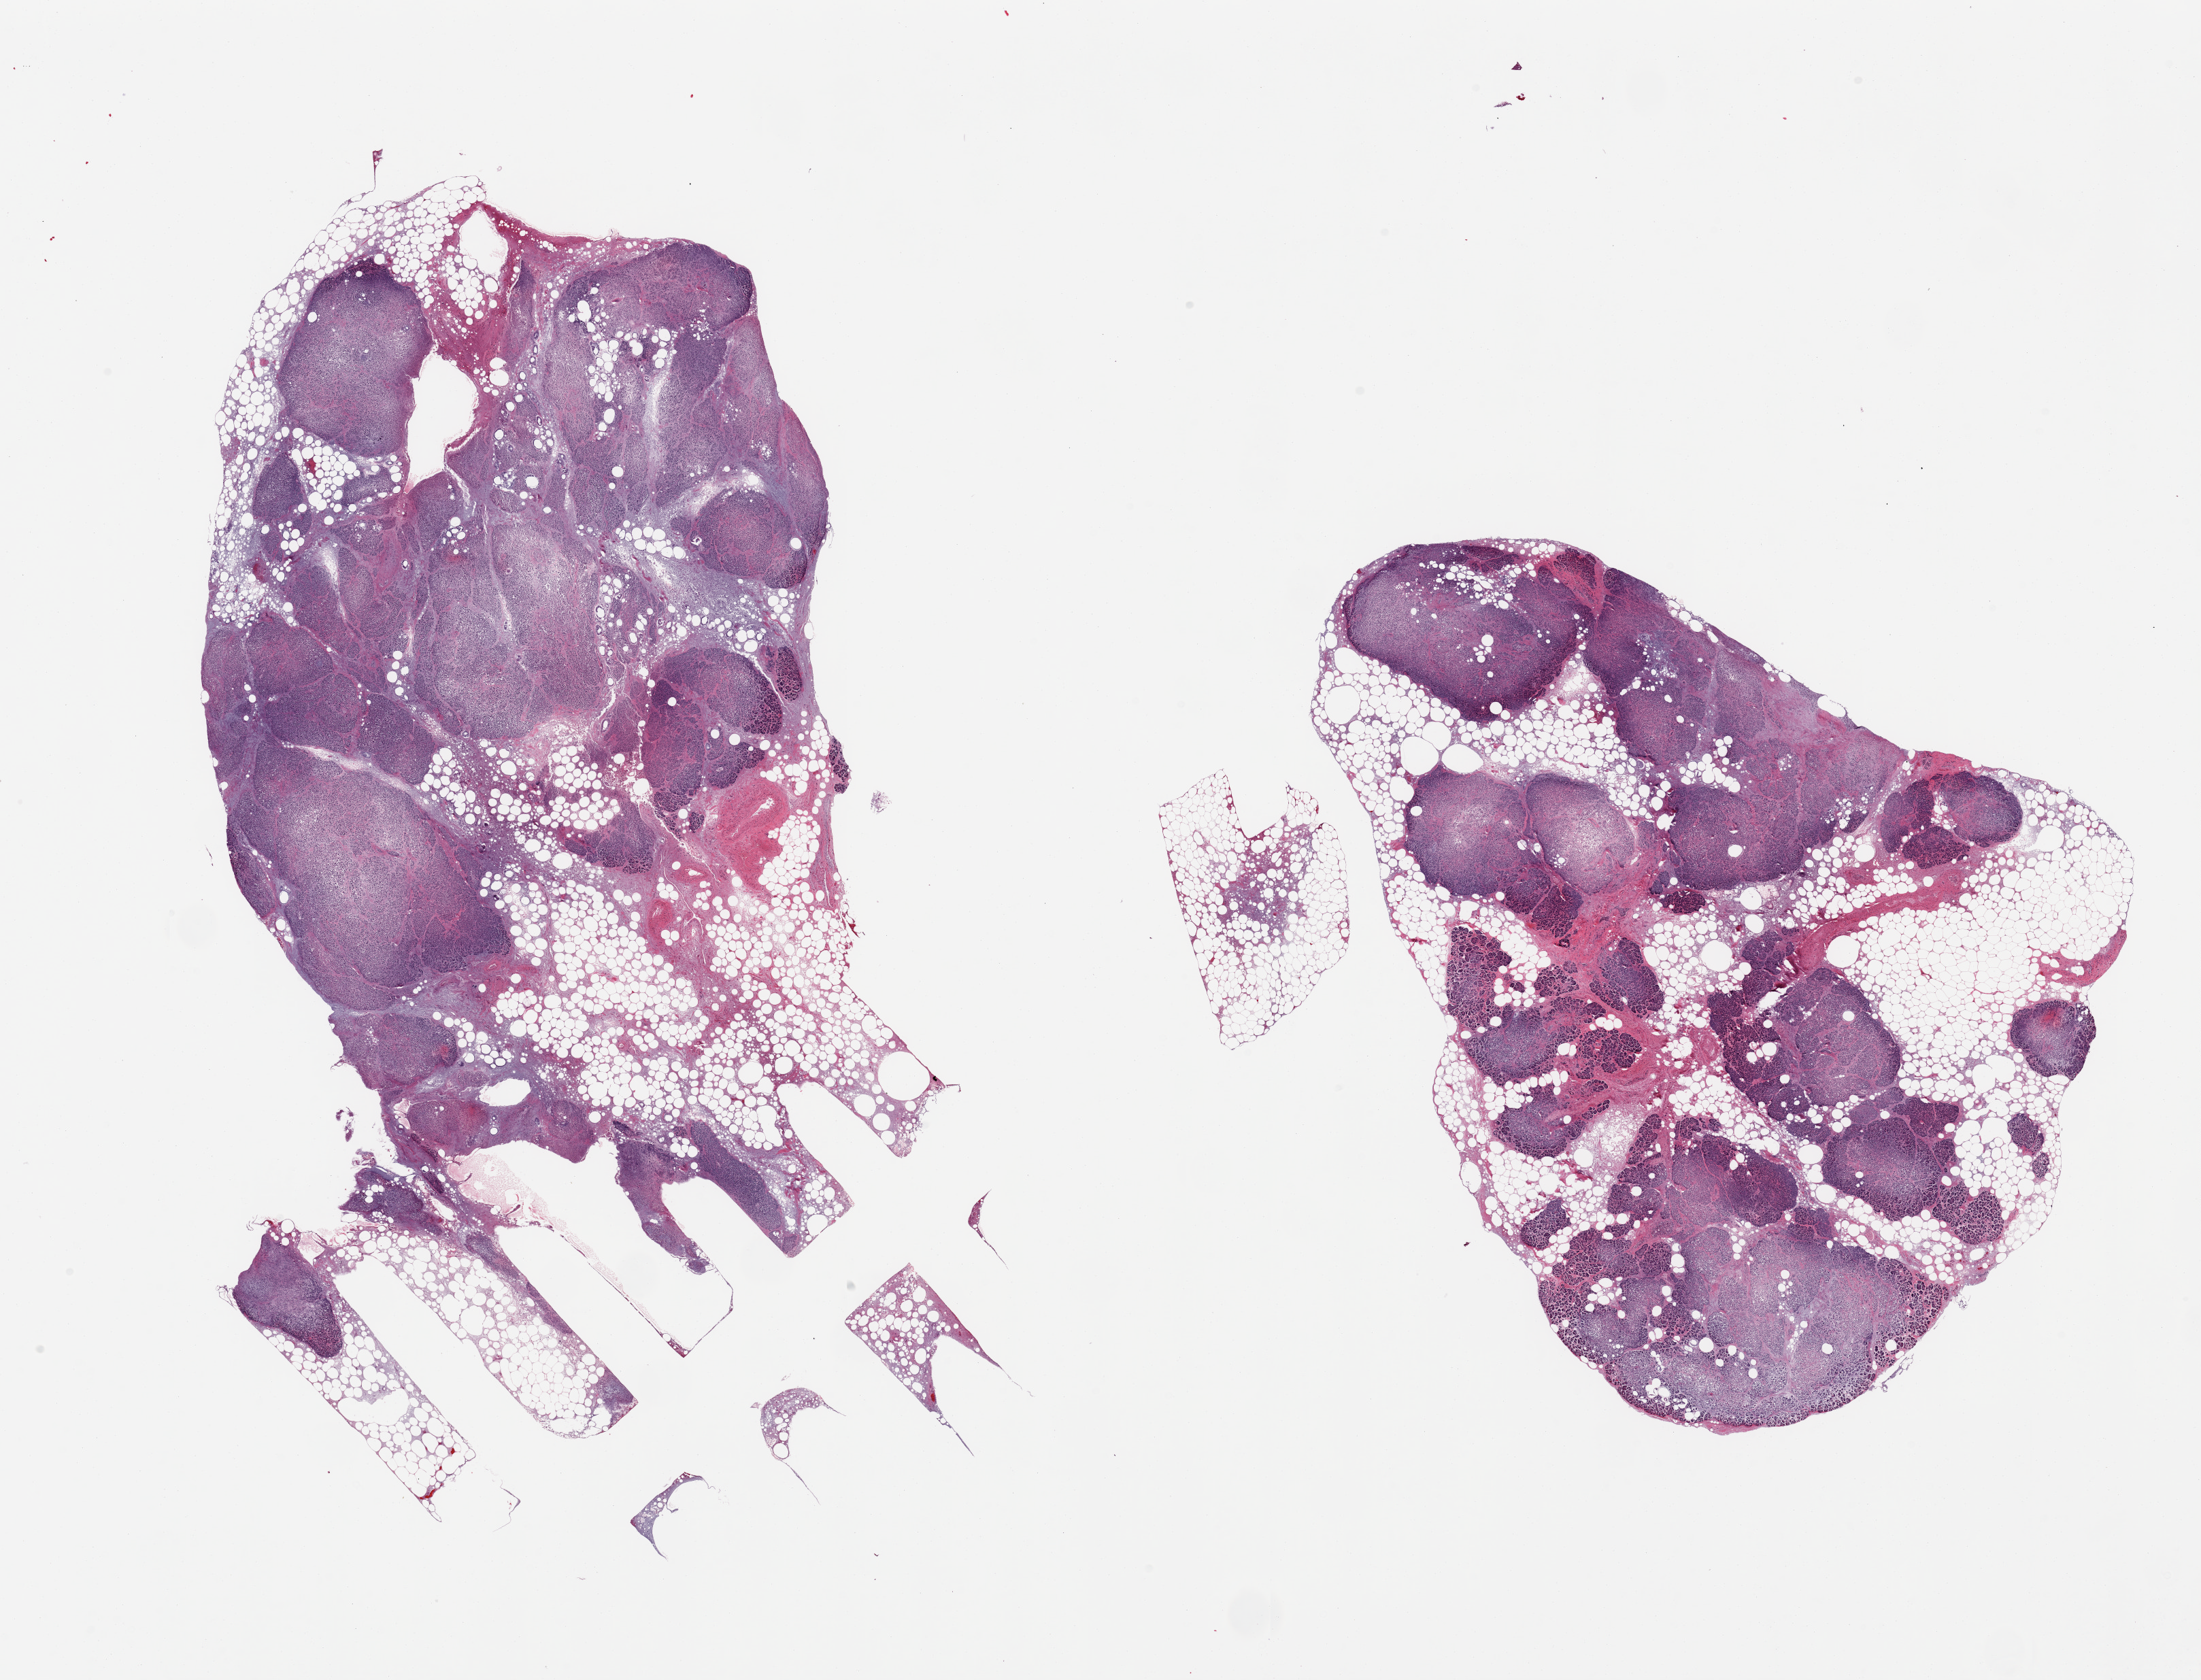
Whole-slide image, hematoxylin and eosin (H&E) stain, brightfield — whole scanned area (about 25.6 x 19.5 mm) shown as a low-resolution overview; PAXgene-fixed, paraffin-embedded tissue; target tissue: pancreas; donor tissue sample. Male donor.
• review note (as recorded): 2 pieces; up to grade 3 parenchymal and septal autolysis; Langerhans islands not preserved; ~50% internal/external fat